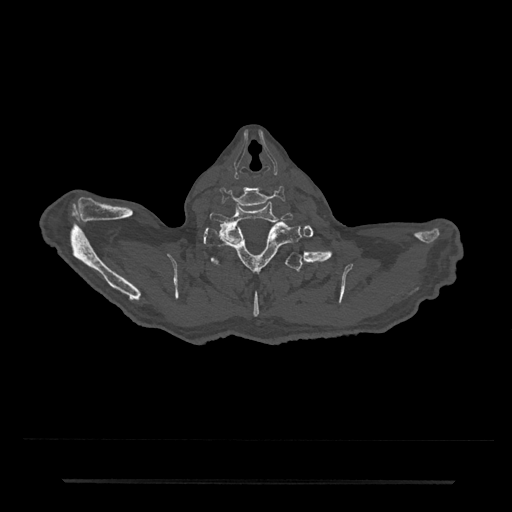
CT including the spine, one axial slice; position 724 of 797 along the scan axis; 120 kVp; bone window (W 1800 / L 400 HU); 0.5 mm slice thickness; 512 × 512 image matrix, field of view 427 × 427 mm. Male patient, age 74 years. Case-level facts recorded for this patient, not image findings: primary cancer: prostate.
Outlined on this slice (semi-automatically segmented with operator editing):
- T1 vertebra: box from (x=203, y=220) to (x=301, y=271) px
- T2 vertebra: (x=211, y=252)–(x=314, y=318)